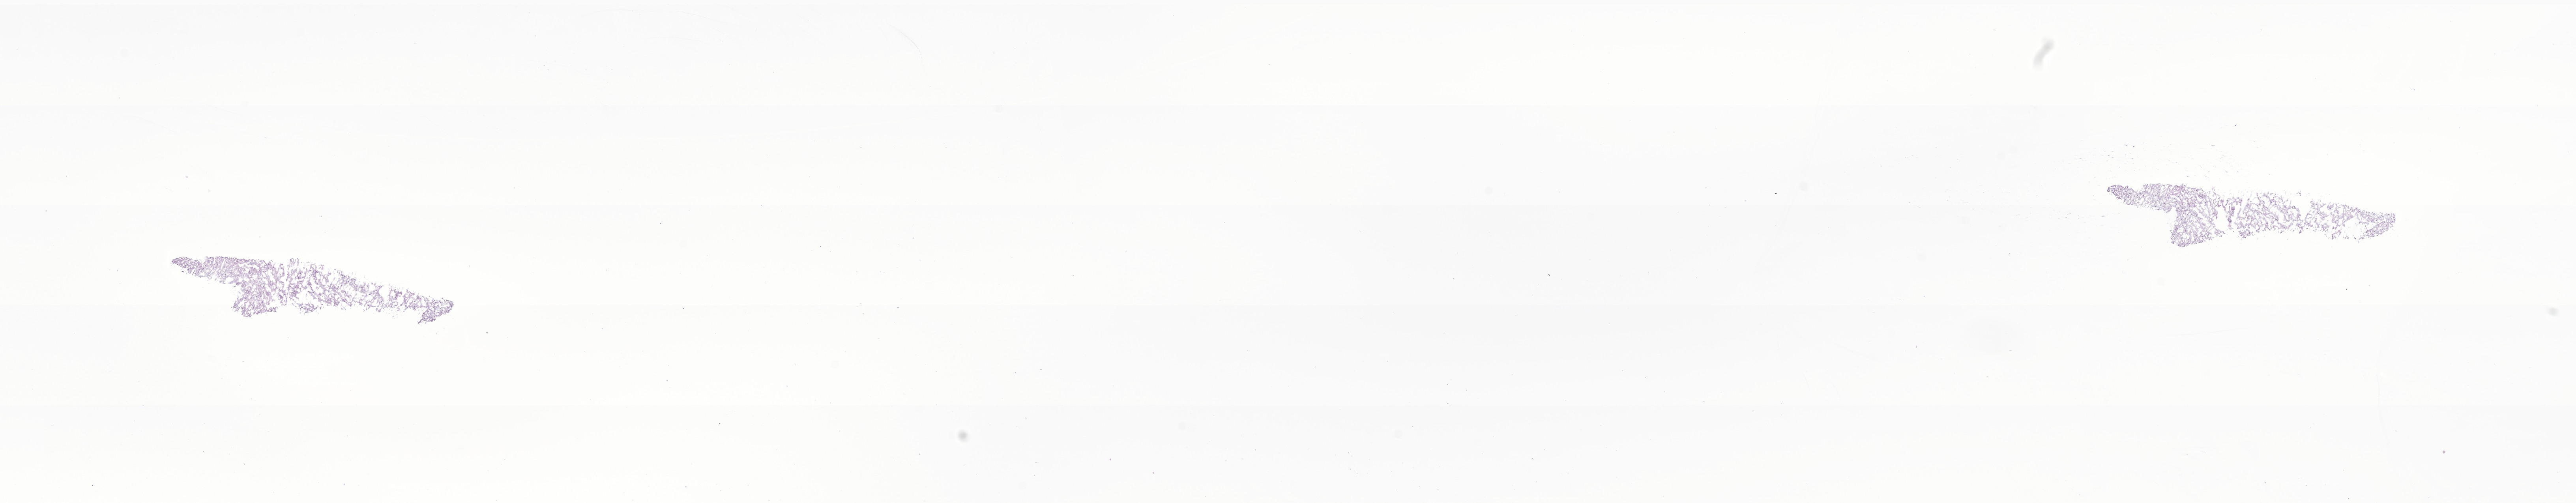
Haematoxylin and eosin whole-slide image of tumor tissue from the temporal lobe, low-resolution overview of the scanned area, about 27.5 x 5.4 mm. Frozen section (OCT-embedded). Patient: female, age 56 months.
Recorded diagnosis: Glioma, malignant.